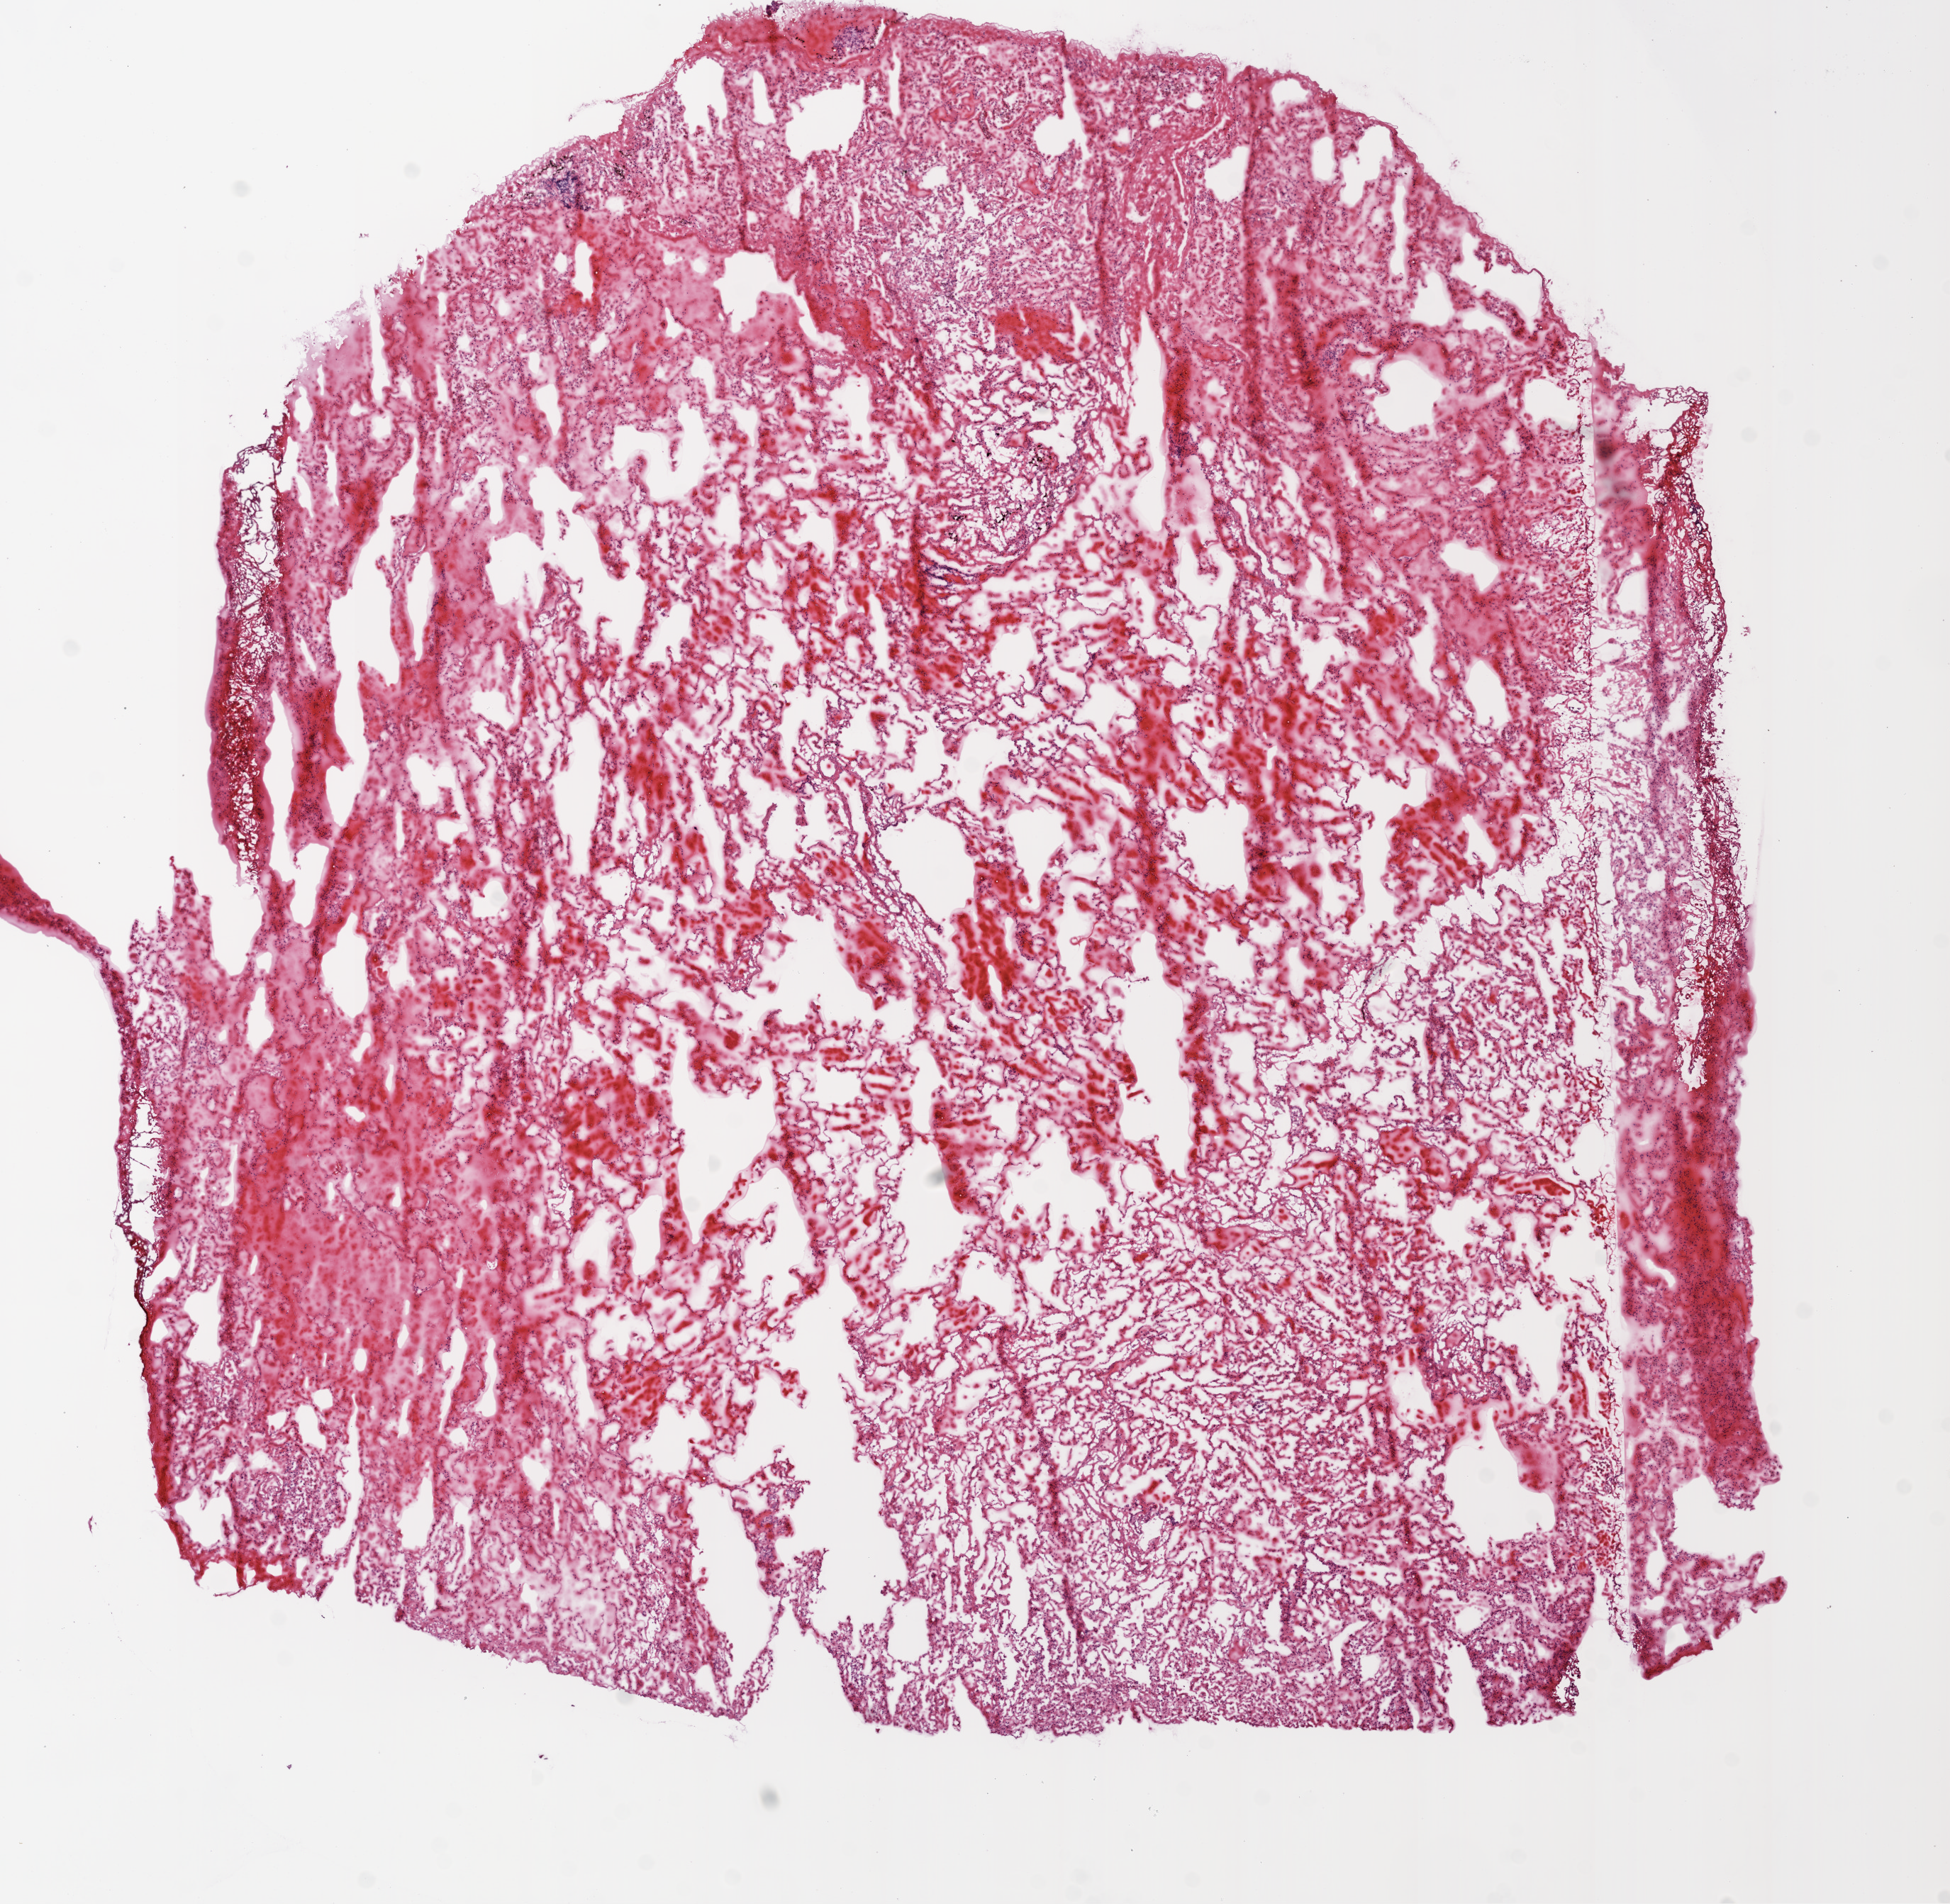
H&E whole-slide image — whole scanned area (about 11.0 x 10.8 mm, acquisition: 20x scan) shown as a low-resolution overview, frozen section from the bottom of the tissue portion, solid tissue normal (non-tumour tissue) sample from the lung. Female, age 52 years at initial diagnosis.
This section: solid tissue normal sample (biorepository sample class). Patient diagnosis: Adenocarcinoma, NOS (upper lobe, lung).